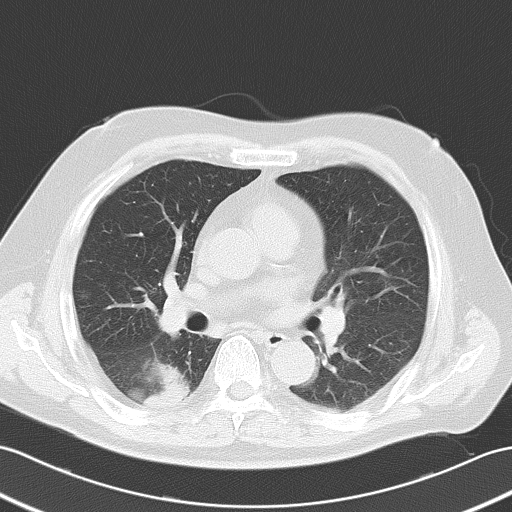
Chest CT, one axial slice. Position 24 of 52 along the scan axis. Reconstruction kernel B70f. 120 kVp. Lung window (W 1500 / L -600 HU). 5 mm slice thickness. 512 × 512 image matrix. Male patient, age 70 years. Case-level facts recorded for this patient, not image findings: clinical TNM (as recorded): T2 N0 M0.
Annotated regions visible in this slice (rectangle marked by the reading radiologist):
- lung tumour (recorded histology: adenocarcinoma): bounding box [x1, y1, x2, y2] px = [128, 356, 192, 418]